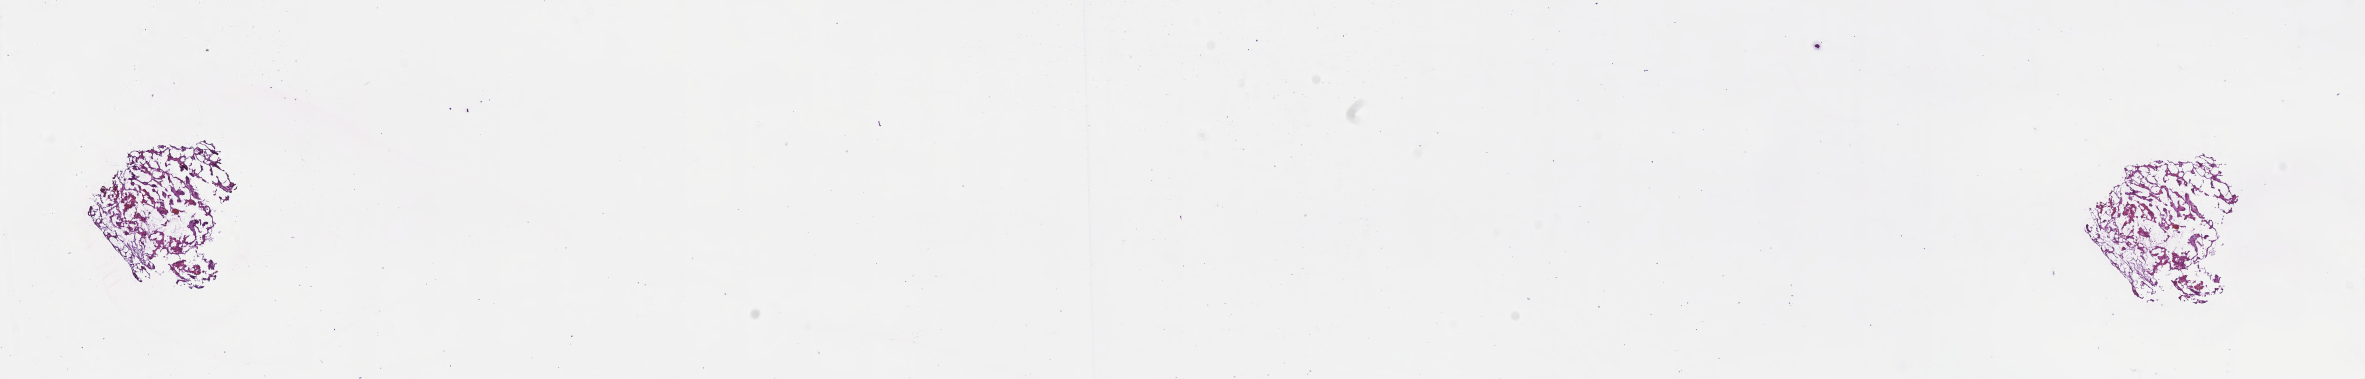
Digitized hematoxylin and eosin (H&E)-stained section of tumor tissue from the brain — whole scanned area (about 19.1 x 3.1 mm) shown as a low-resolution overview, frozen section. Patient male; age 121 months (10 years 1 month).
Diagnosis: Pilocytic astrocytoma.